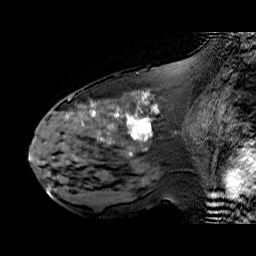
Breast MRI (dynamic contrast-enhanced), one sagittal slice; position 30 of 60 along the scan axis; dynamic contrast-enhanced series, time point 2 of 6 at this slice position (early post-contrast); 1.5 T; TE 6.3 ms, TR 32.9 ms; 4 mm slice thickness; 256 × 256 image matrix, field of view 200 × 200 mm. Female patient. Case-level facts recorded for this patient, not image findings: setting: breast cancer imaged before/during neoadjuvant chemotherapy; receptor status: HER2-positive.
Structures marked on this image (semi-automatically segmented with operator editing):
- analysis volume of interest (the breast-tissue region the enhancement analysis was run in; not a lesion): bounding box <48,92,195,174> (left, top, right, bottom; pixels)
- tumour enhancement mask (voxels above the 100 % enhancement threshold inside the analysis volume of interest): <65,92,149,140>